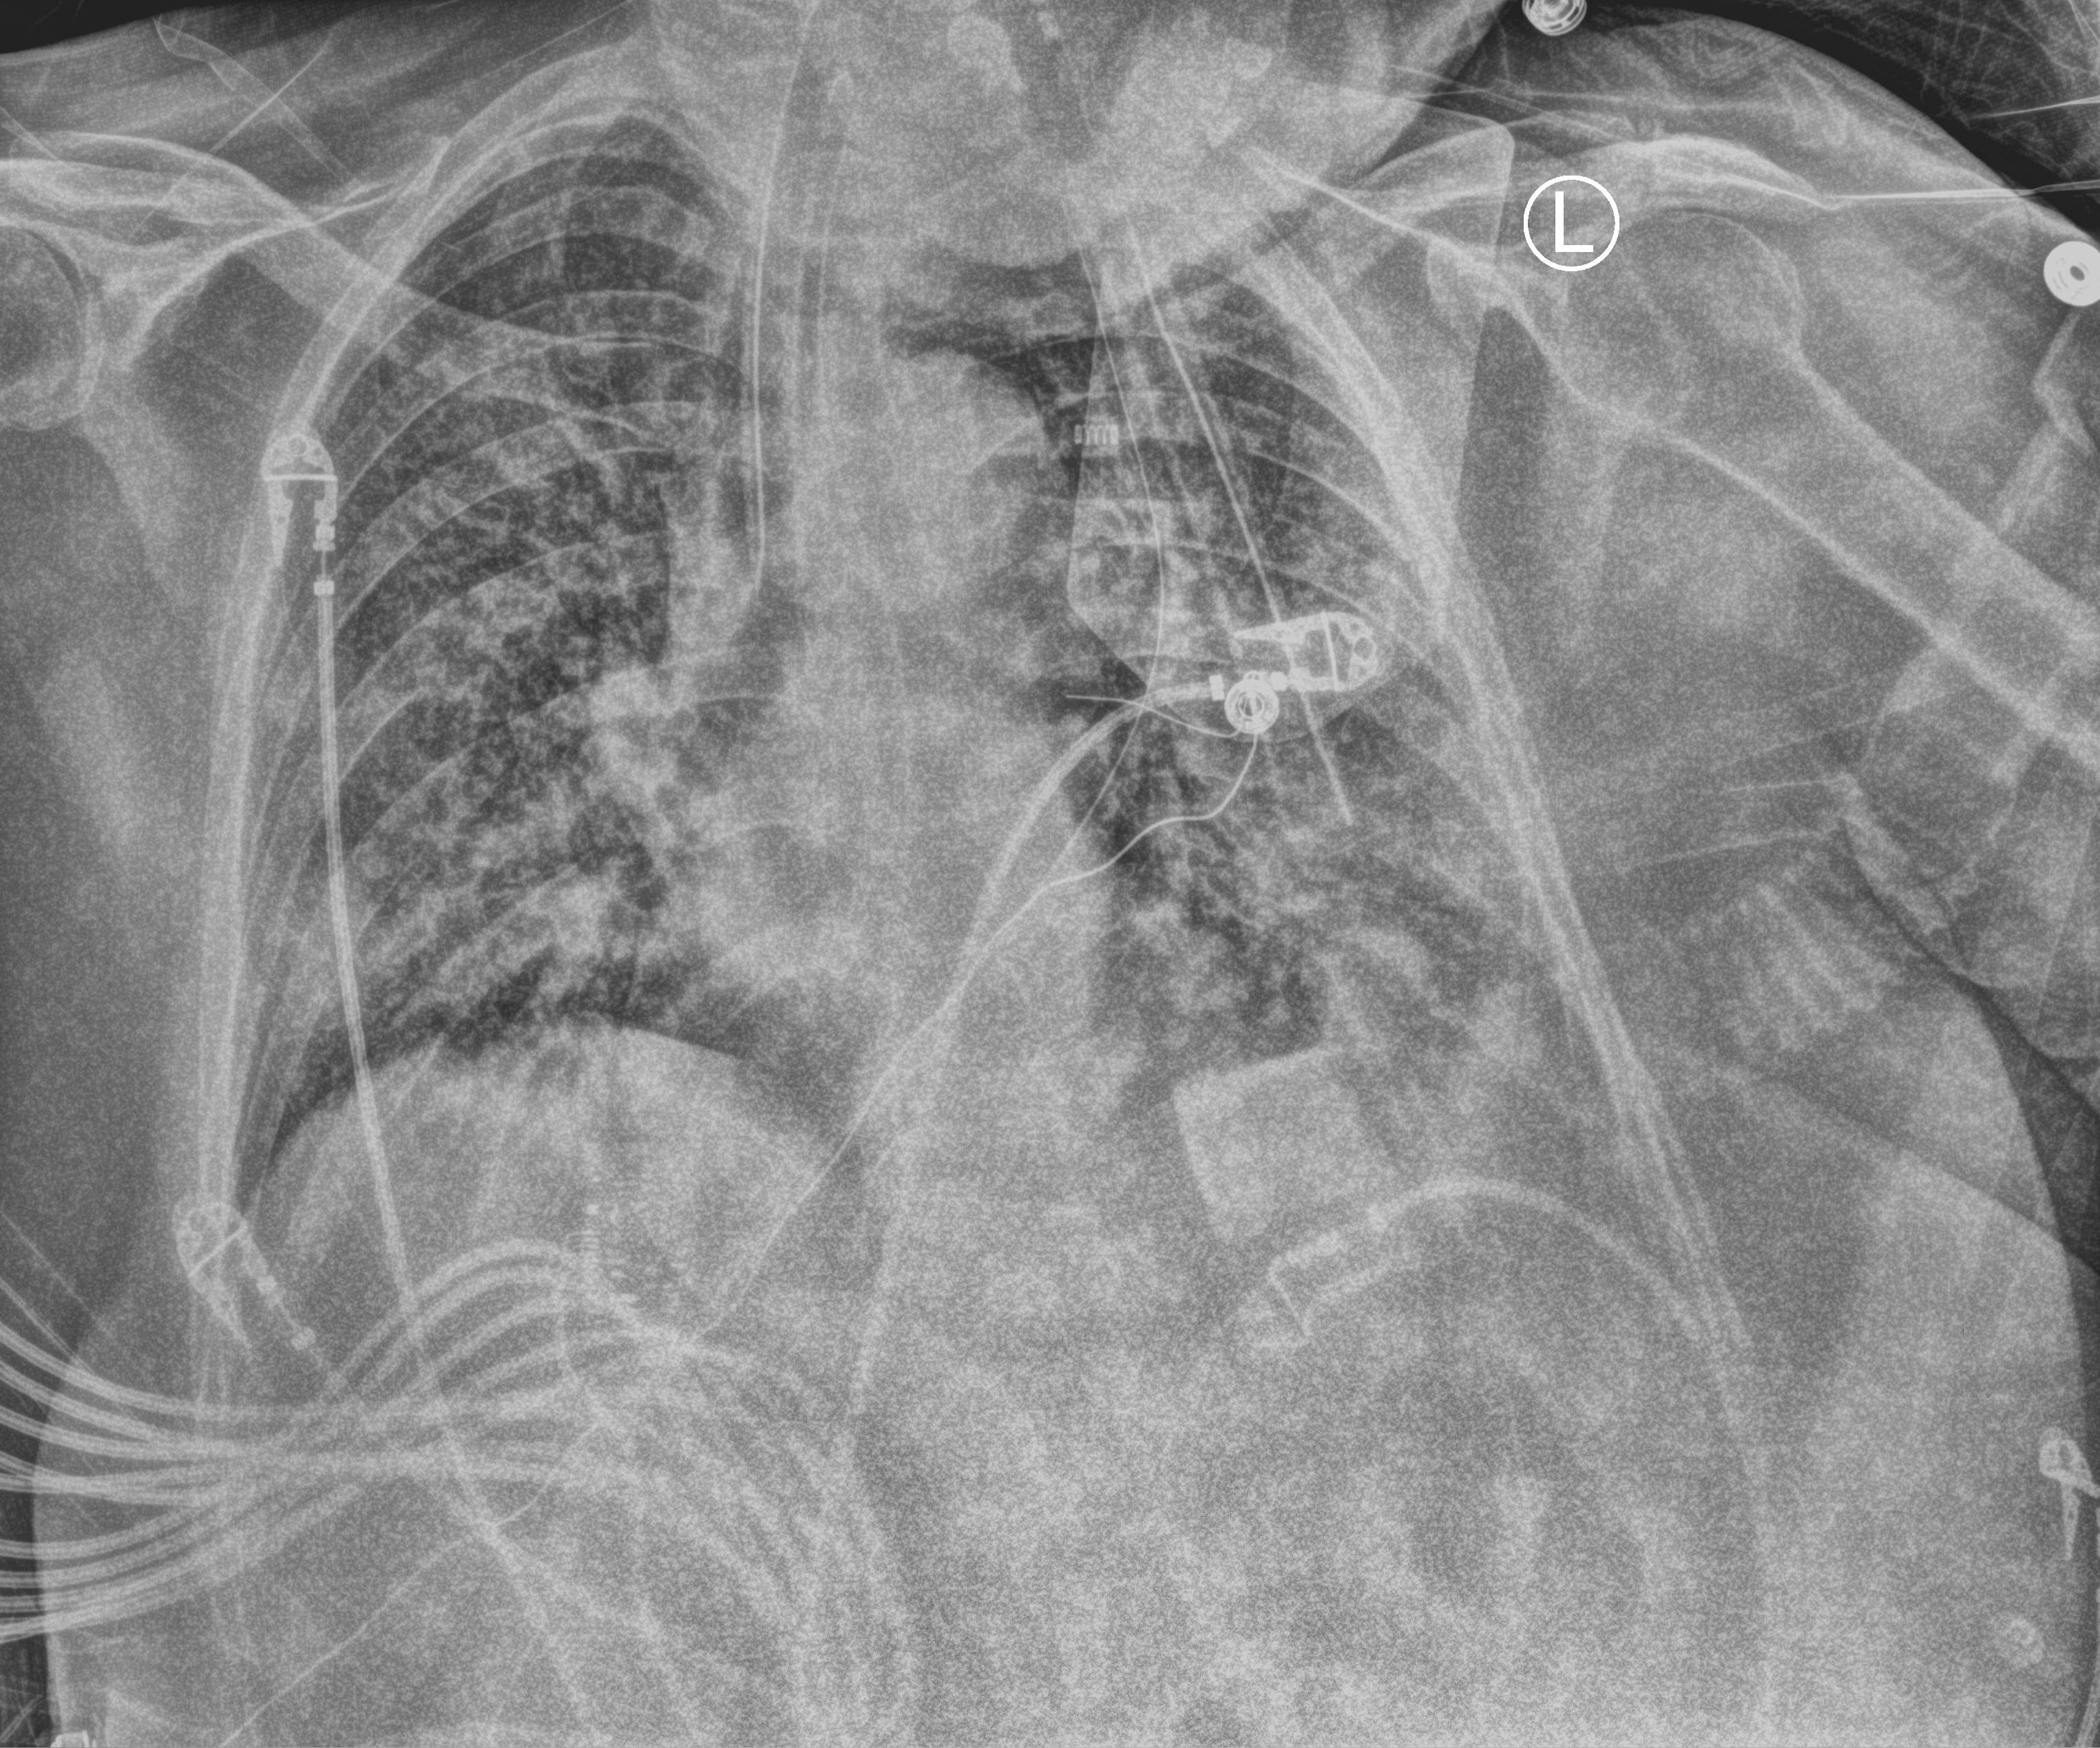
Portable chest radiograph, anteroposterior (AP) projection. Female patient hospitalised with COVID-19, age 60–74 years.
Admission-level facts for this patient (not findings on this image; timing relative to this image not recorded):
- mechanically ventilated during this hospital stay: yes
- other chronic lung disease (admission record): no
- admitted to intensive care during this hospital stay: yes